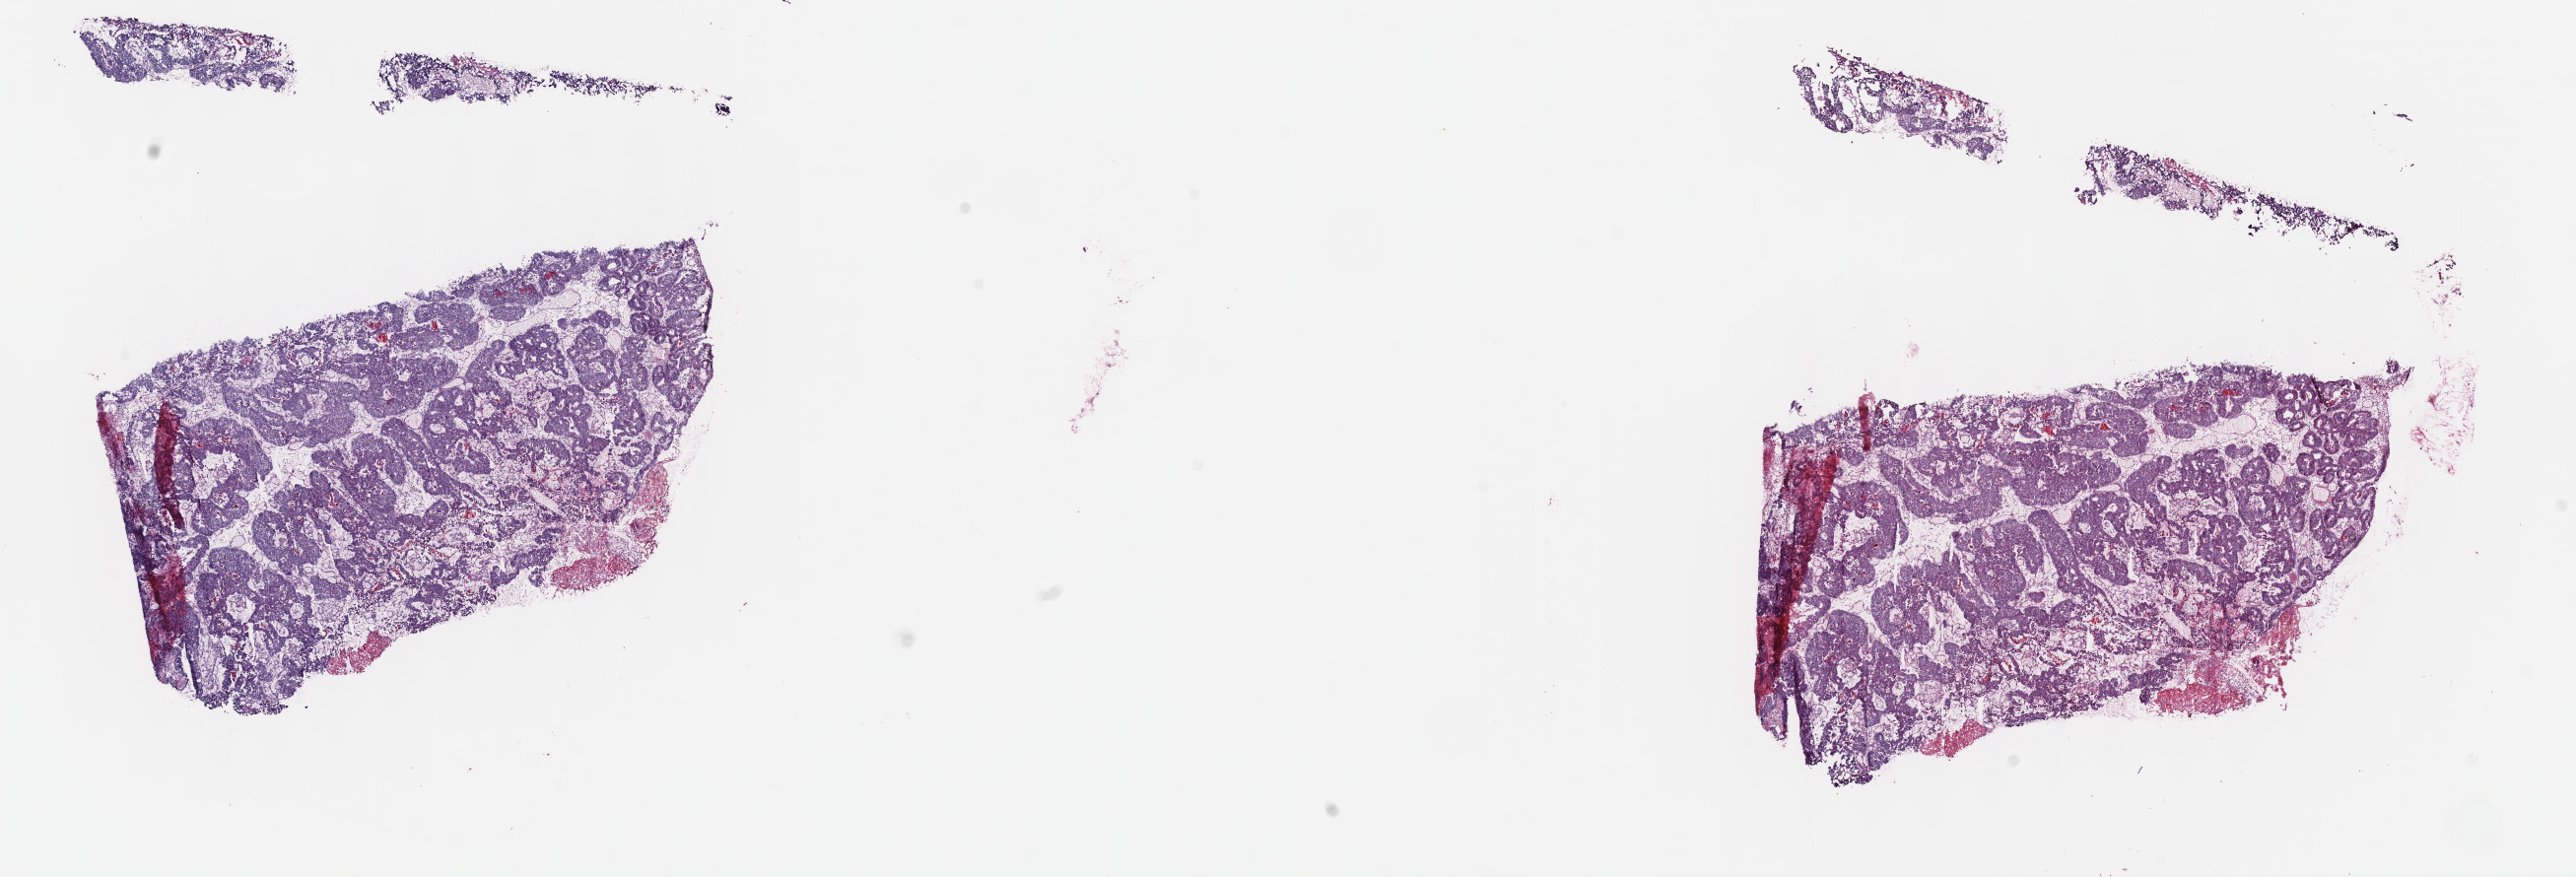
H&E whole-slide image — low-resolution overview of the scanned area, about 21.1 x 7.2 mm (acquisition: 40x scan), frozen section, sample: primary tumour, colon. Patient: female, age at initial diagnosis 44 years. Composition of this section per pathologist review: tumour cells 90%, tumour nuclei 70%, normal cells 0%, stromal cells 0%, necrosis 10%. Infiltration values recorded for this section: lymphocyte infiltration 5%, monocyte infiltration 2%, neutrophil infiltration 2%.
Histologic diagnosis: Adenocarcinoma, NOS (cecum). AJCC pathologic stage: IIB (7th edition).